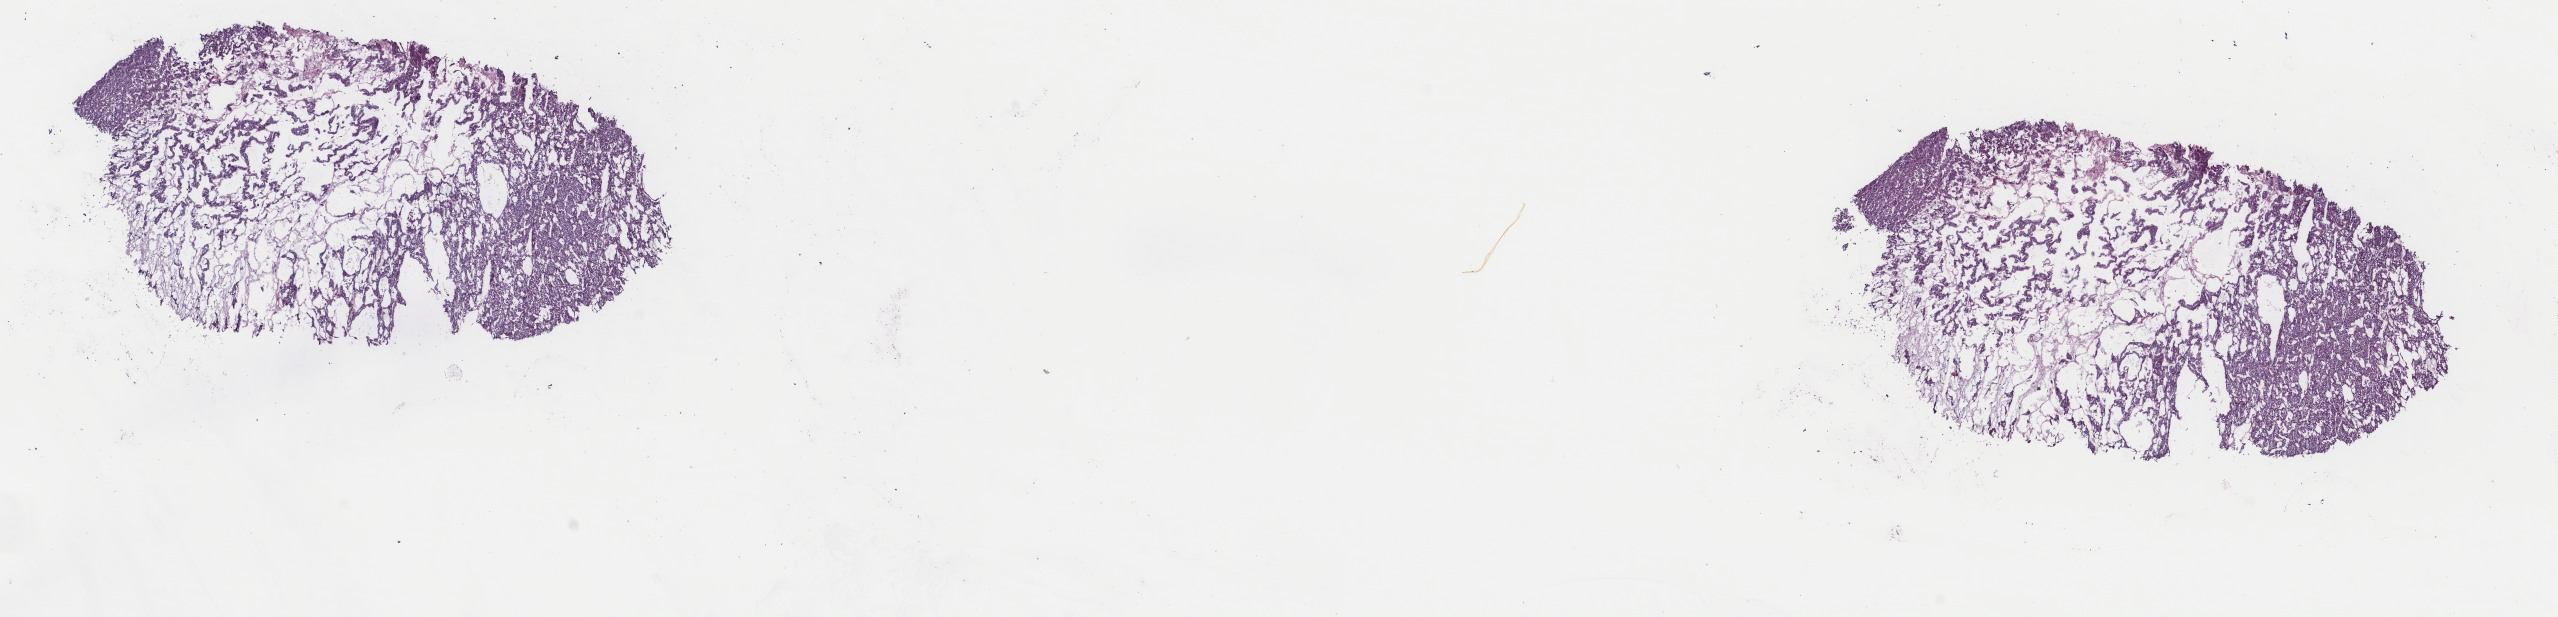
Whole-slide histology image, H&E — shown as a low-resolution overview of the whole scanned area (about 20.3 x 4.9 mm); frozen section from the top of the tissue portion; kidney, primary tumour sample. Patient: female, age at initial diagnosis 75 years. Composition of this section per pathologist review: tumour cells 100%, tumour nuclei 80%, normal cells 0%, stromal cells 0%, necrosis 0%. Infiltration values recorded for this section: lymphocyte infiltration 1%, monocyte infiltration 0%, neutrophil infiltration 0%.
TNM: T1a NX MX. AJCC pathologic stage: I (7th edition). Pathologic diagnosis: Renal cell carcinoma, chromophobe type. Laterality: left.